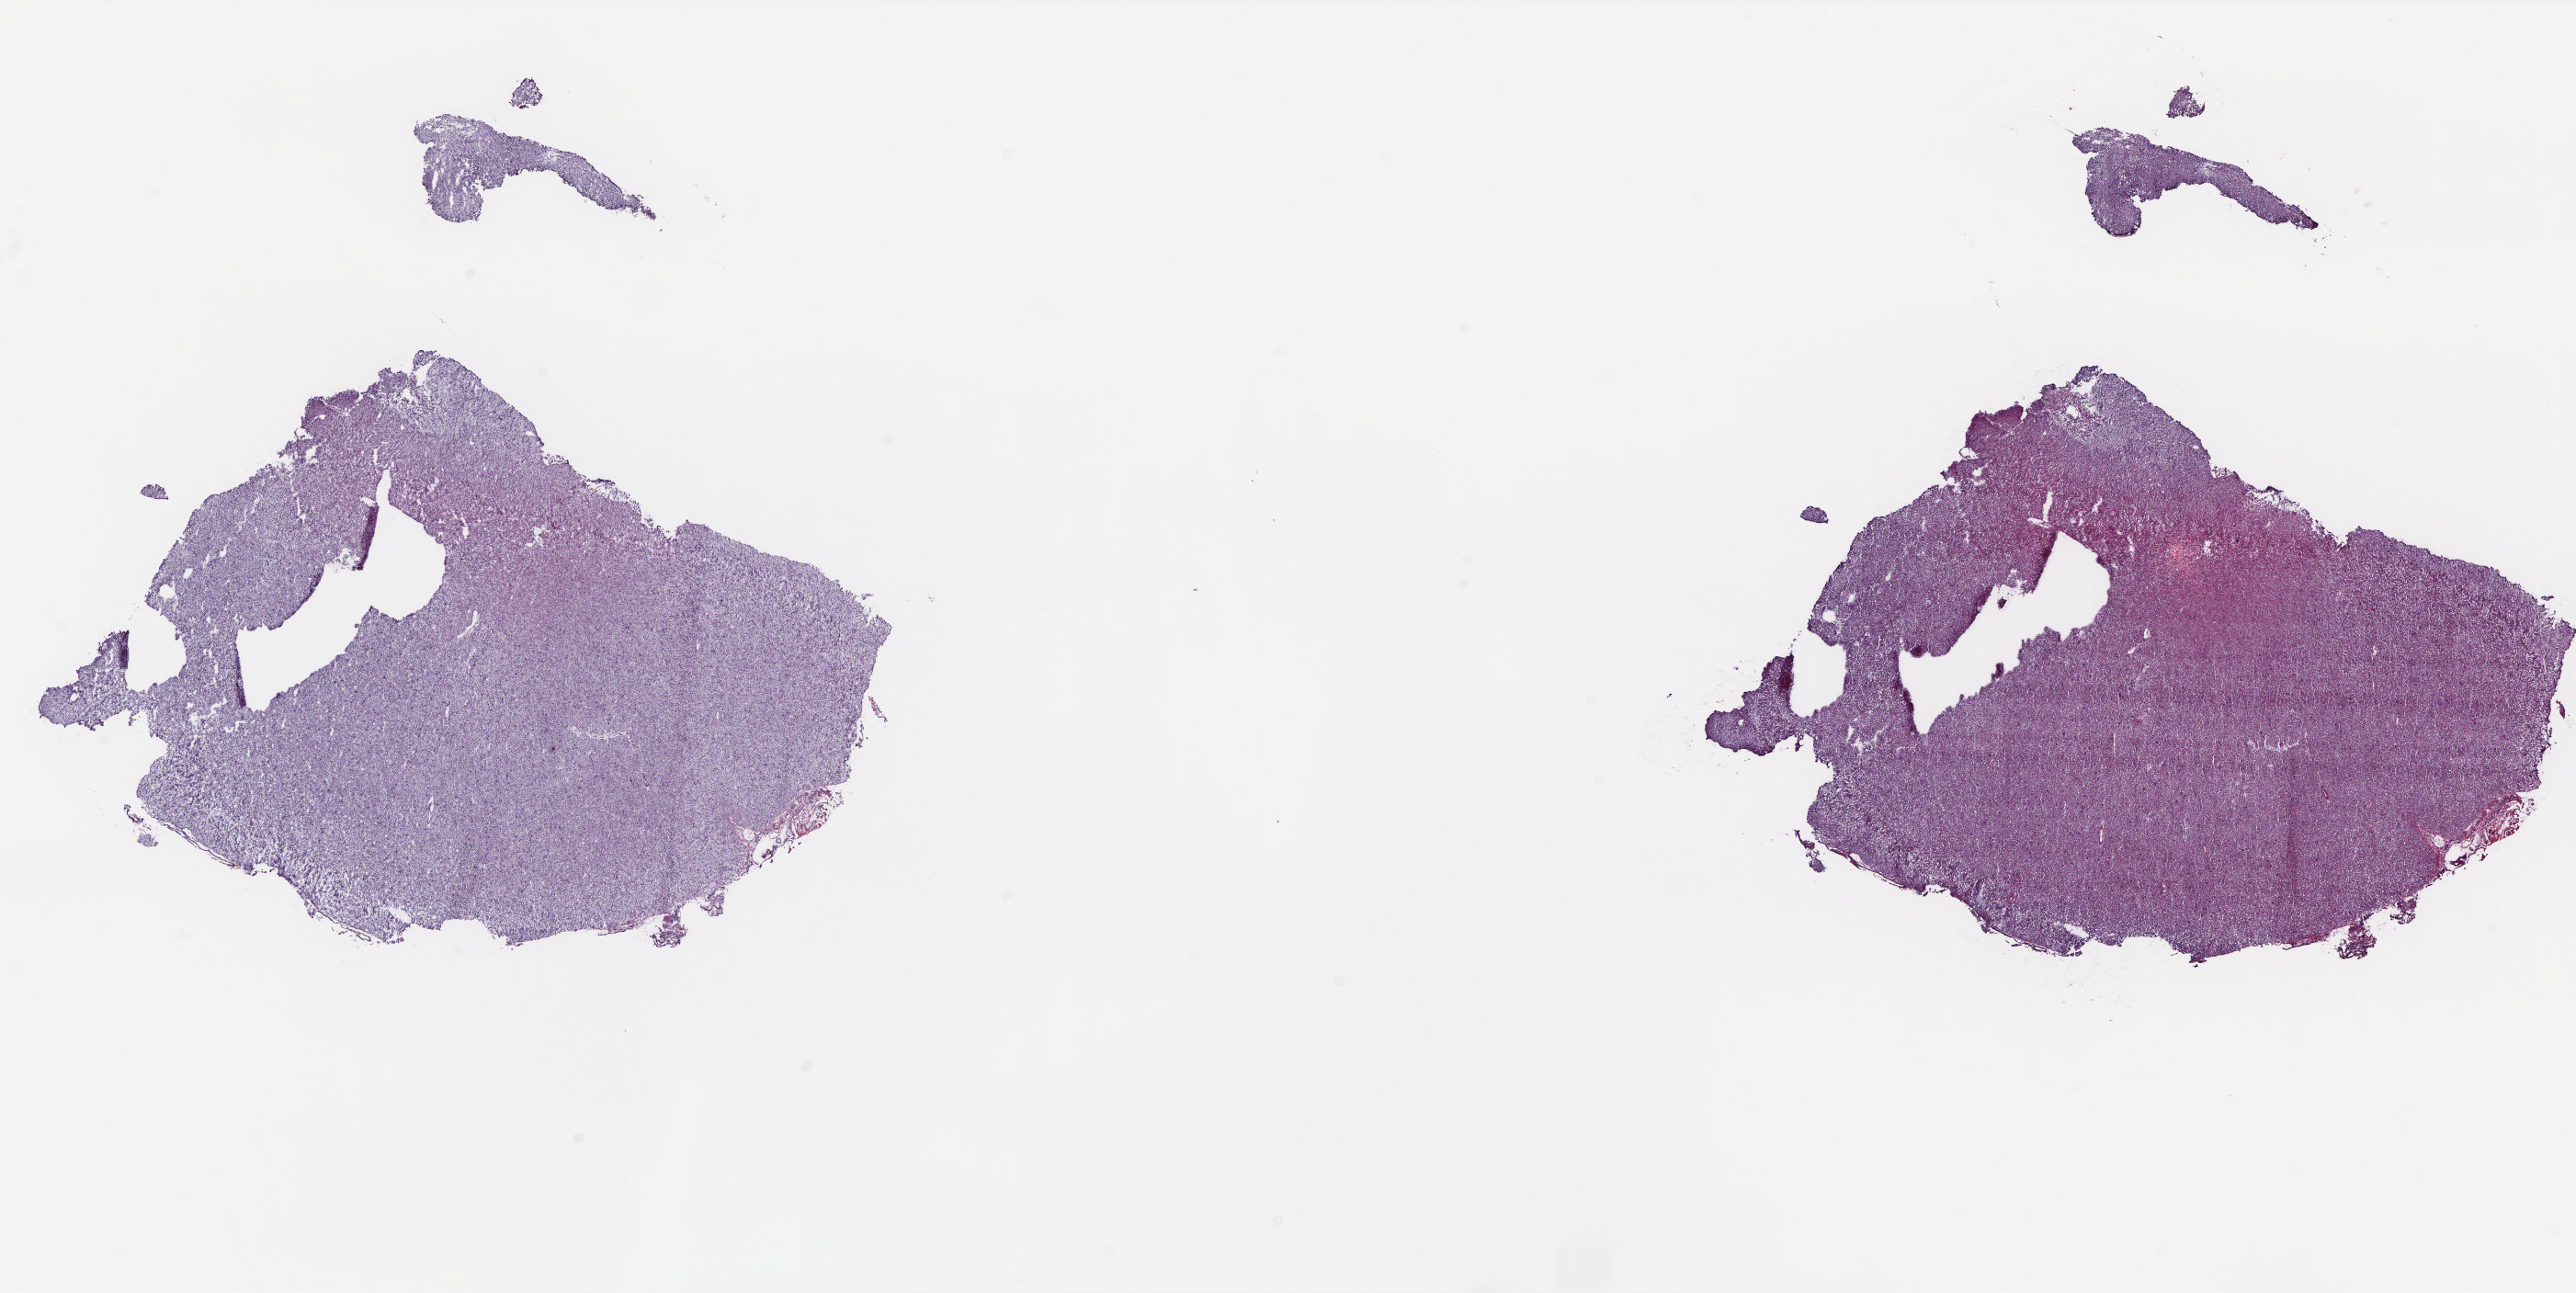
Hematoxylin and eosin (H&E) stained whole-slide image — low-resolution overview of the scanned area, about 22.6 x 11.3 mm (slide scanned at 20x). Frozen section from the top of the tissue portion. Brain, solid tissue normal (non-tumour tissue) sample. Slide review estimates, as recorded: tumour cells 0%, tumour nuclei 0%, normal cells 25%, stromal cells 75%, necrosis 0%. Infiltration values recorded for this section: lymphocyte infiltration 0%, monocyte infiltration 0%, neutrophil infiltration 0%.
This section: solid tissue normal (non-tumour) sample.